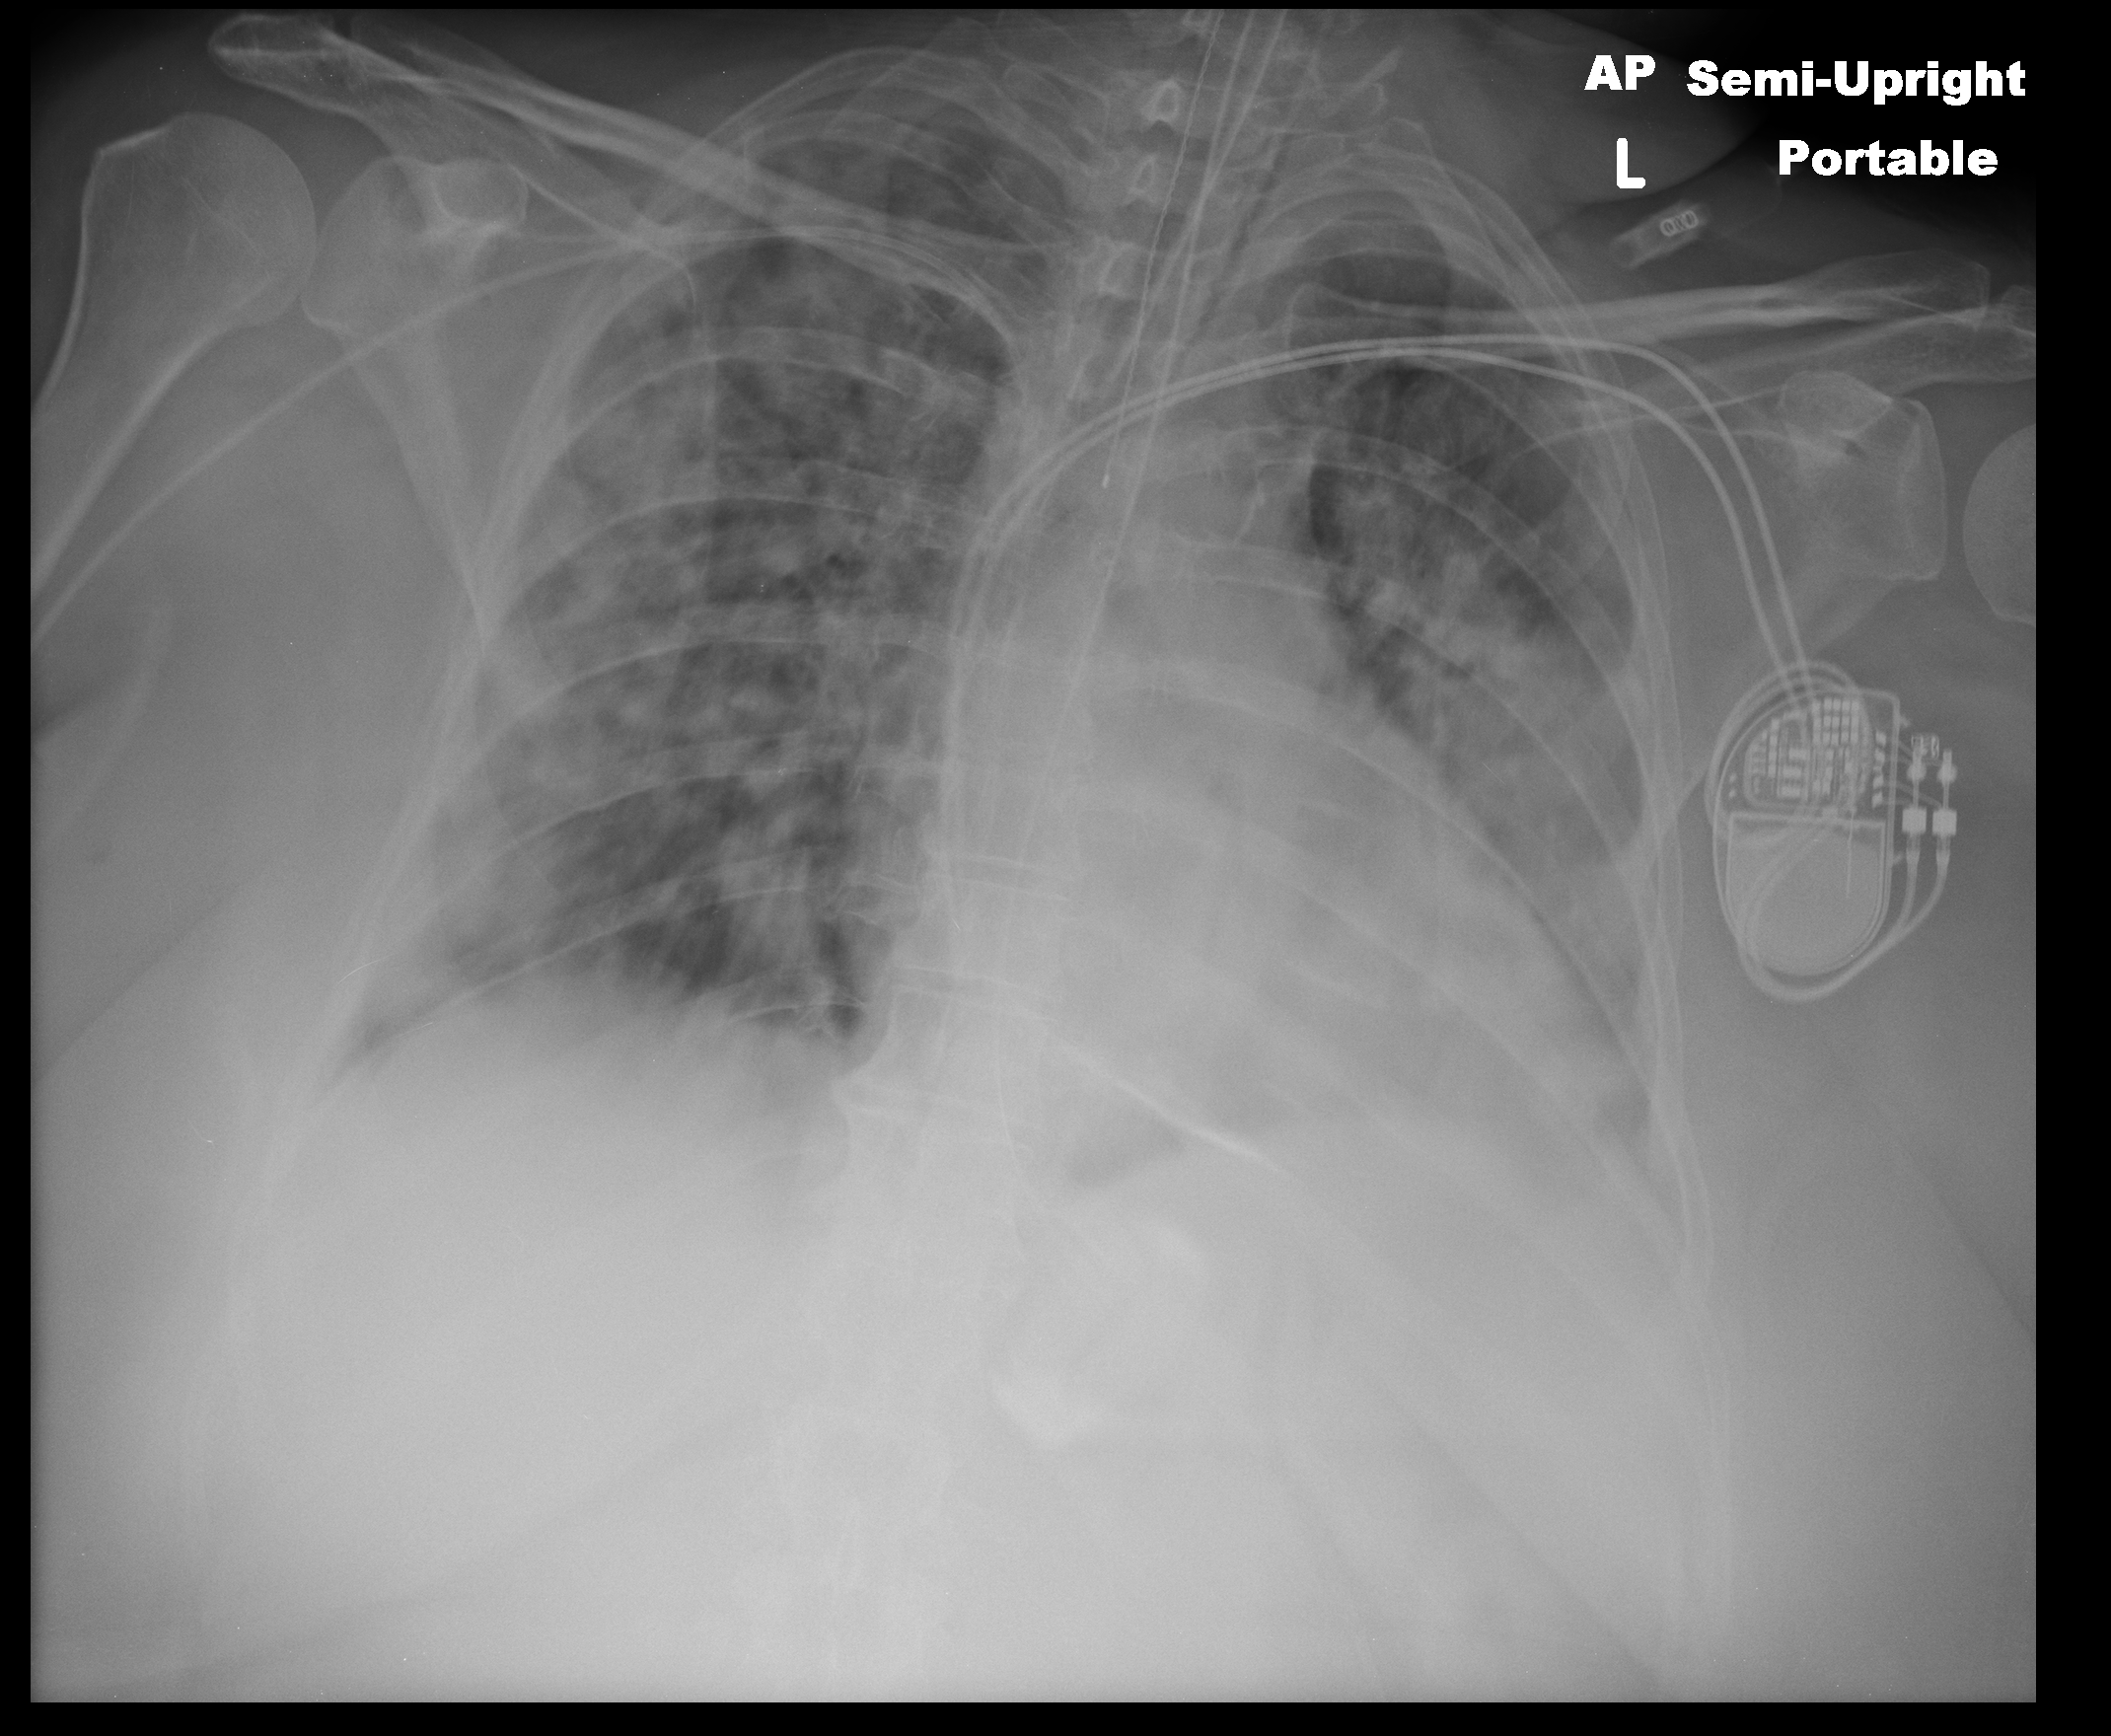
Portable chest radiograph, AP projection. Female patient, age 57 years; imaged 11 days after the COVID-19 diagnosis.
Radiologist key findings (as recorded): Multifocal consolidation and or atelectasis most significantly involving the lingula/left lower lobe. Small left pleural effusion.